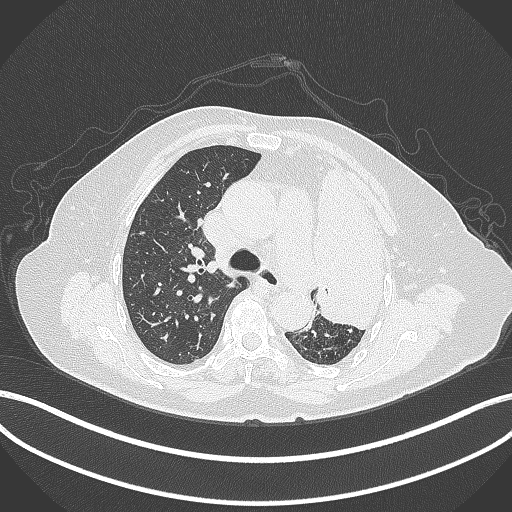
Chest CT, one axial slice; slice 263 of 399 in the series (ordered by position); lung window (W 1500 / L -600 HU); 1 mm slice thickness; 512 × 512 image matrix, field of view 400 × 400 mm. Female patient, age 75 years. Case-level facts recorded for this patient, not image findings: clinical TNM (as recorded): T3 N3 M1.
Outlined on this slice (bounding box drawn by a radiologist):
- lung tumour (recorded histology: adenocarcinoma): box from (x=312, y=164) to (x=401, y=332) px